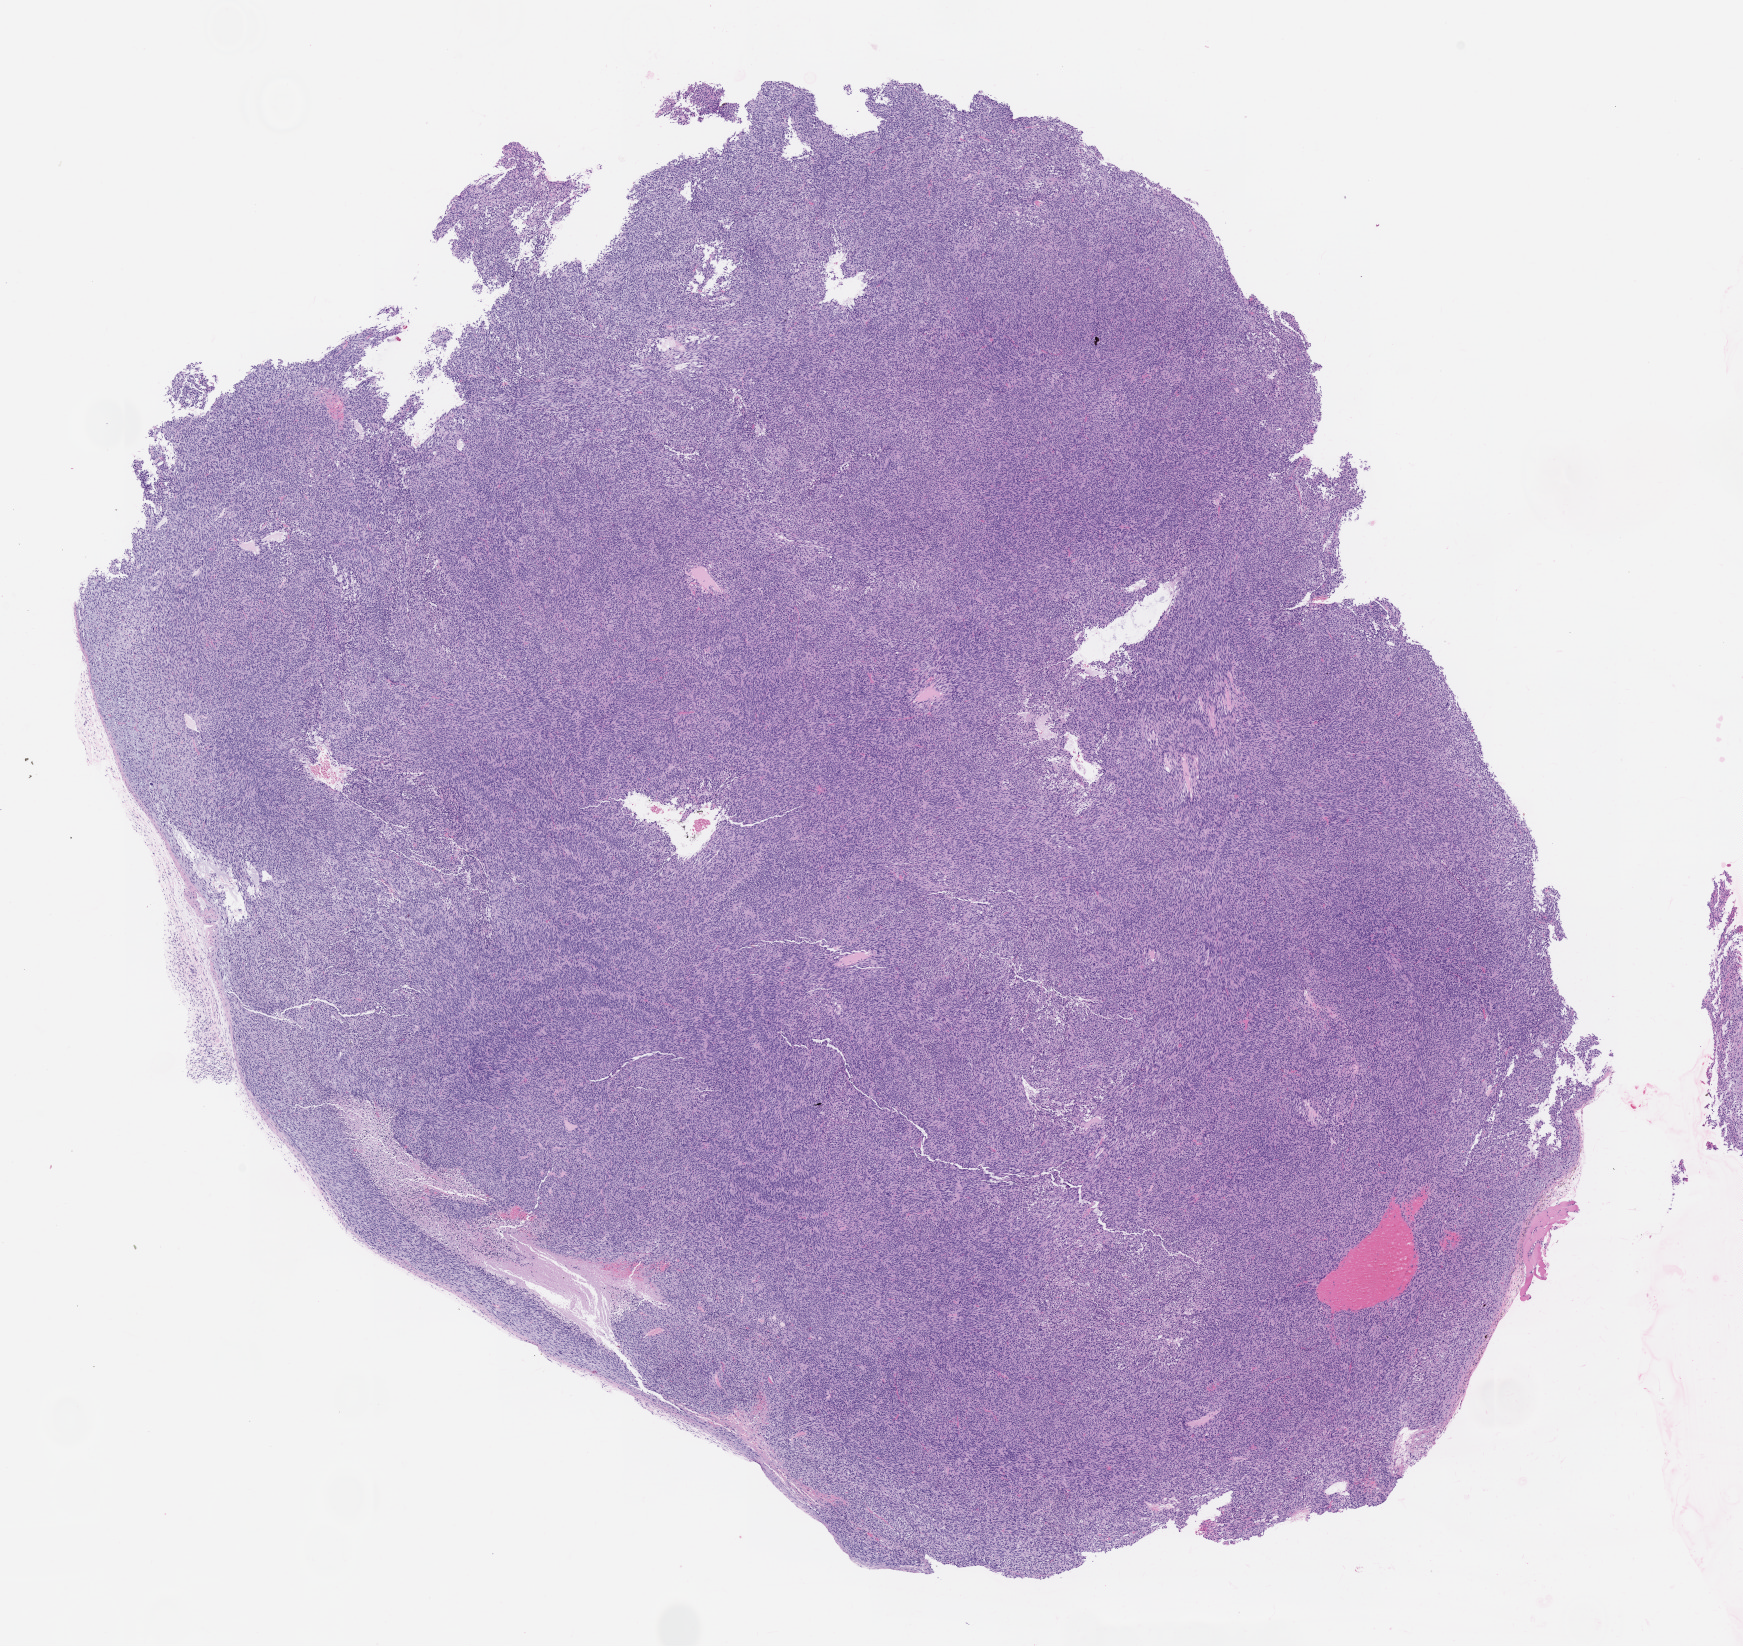
Whole-slide image, haematoxylin and eosin: patient-derived xenograft (human tumor grown in a mouse), passage 2 — a low-resolution overview of the entire scanned area, about 14.0 x 13.2 mm. Formalin-fixed paraffin-embedded section. Originating tumor site category: uterus.
Originating patient diagnosis: Leiomyosarcoma.